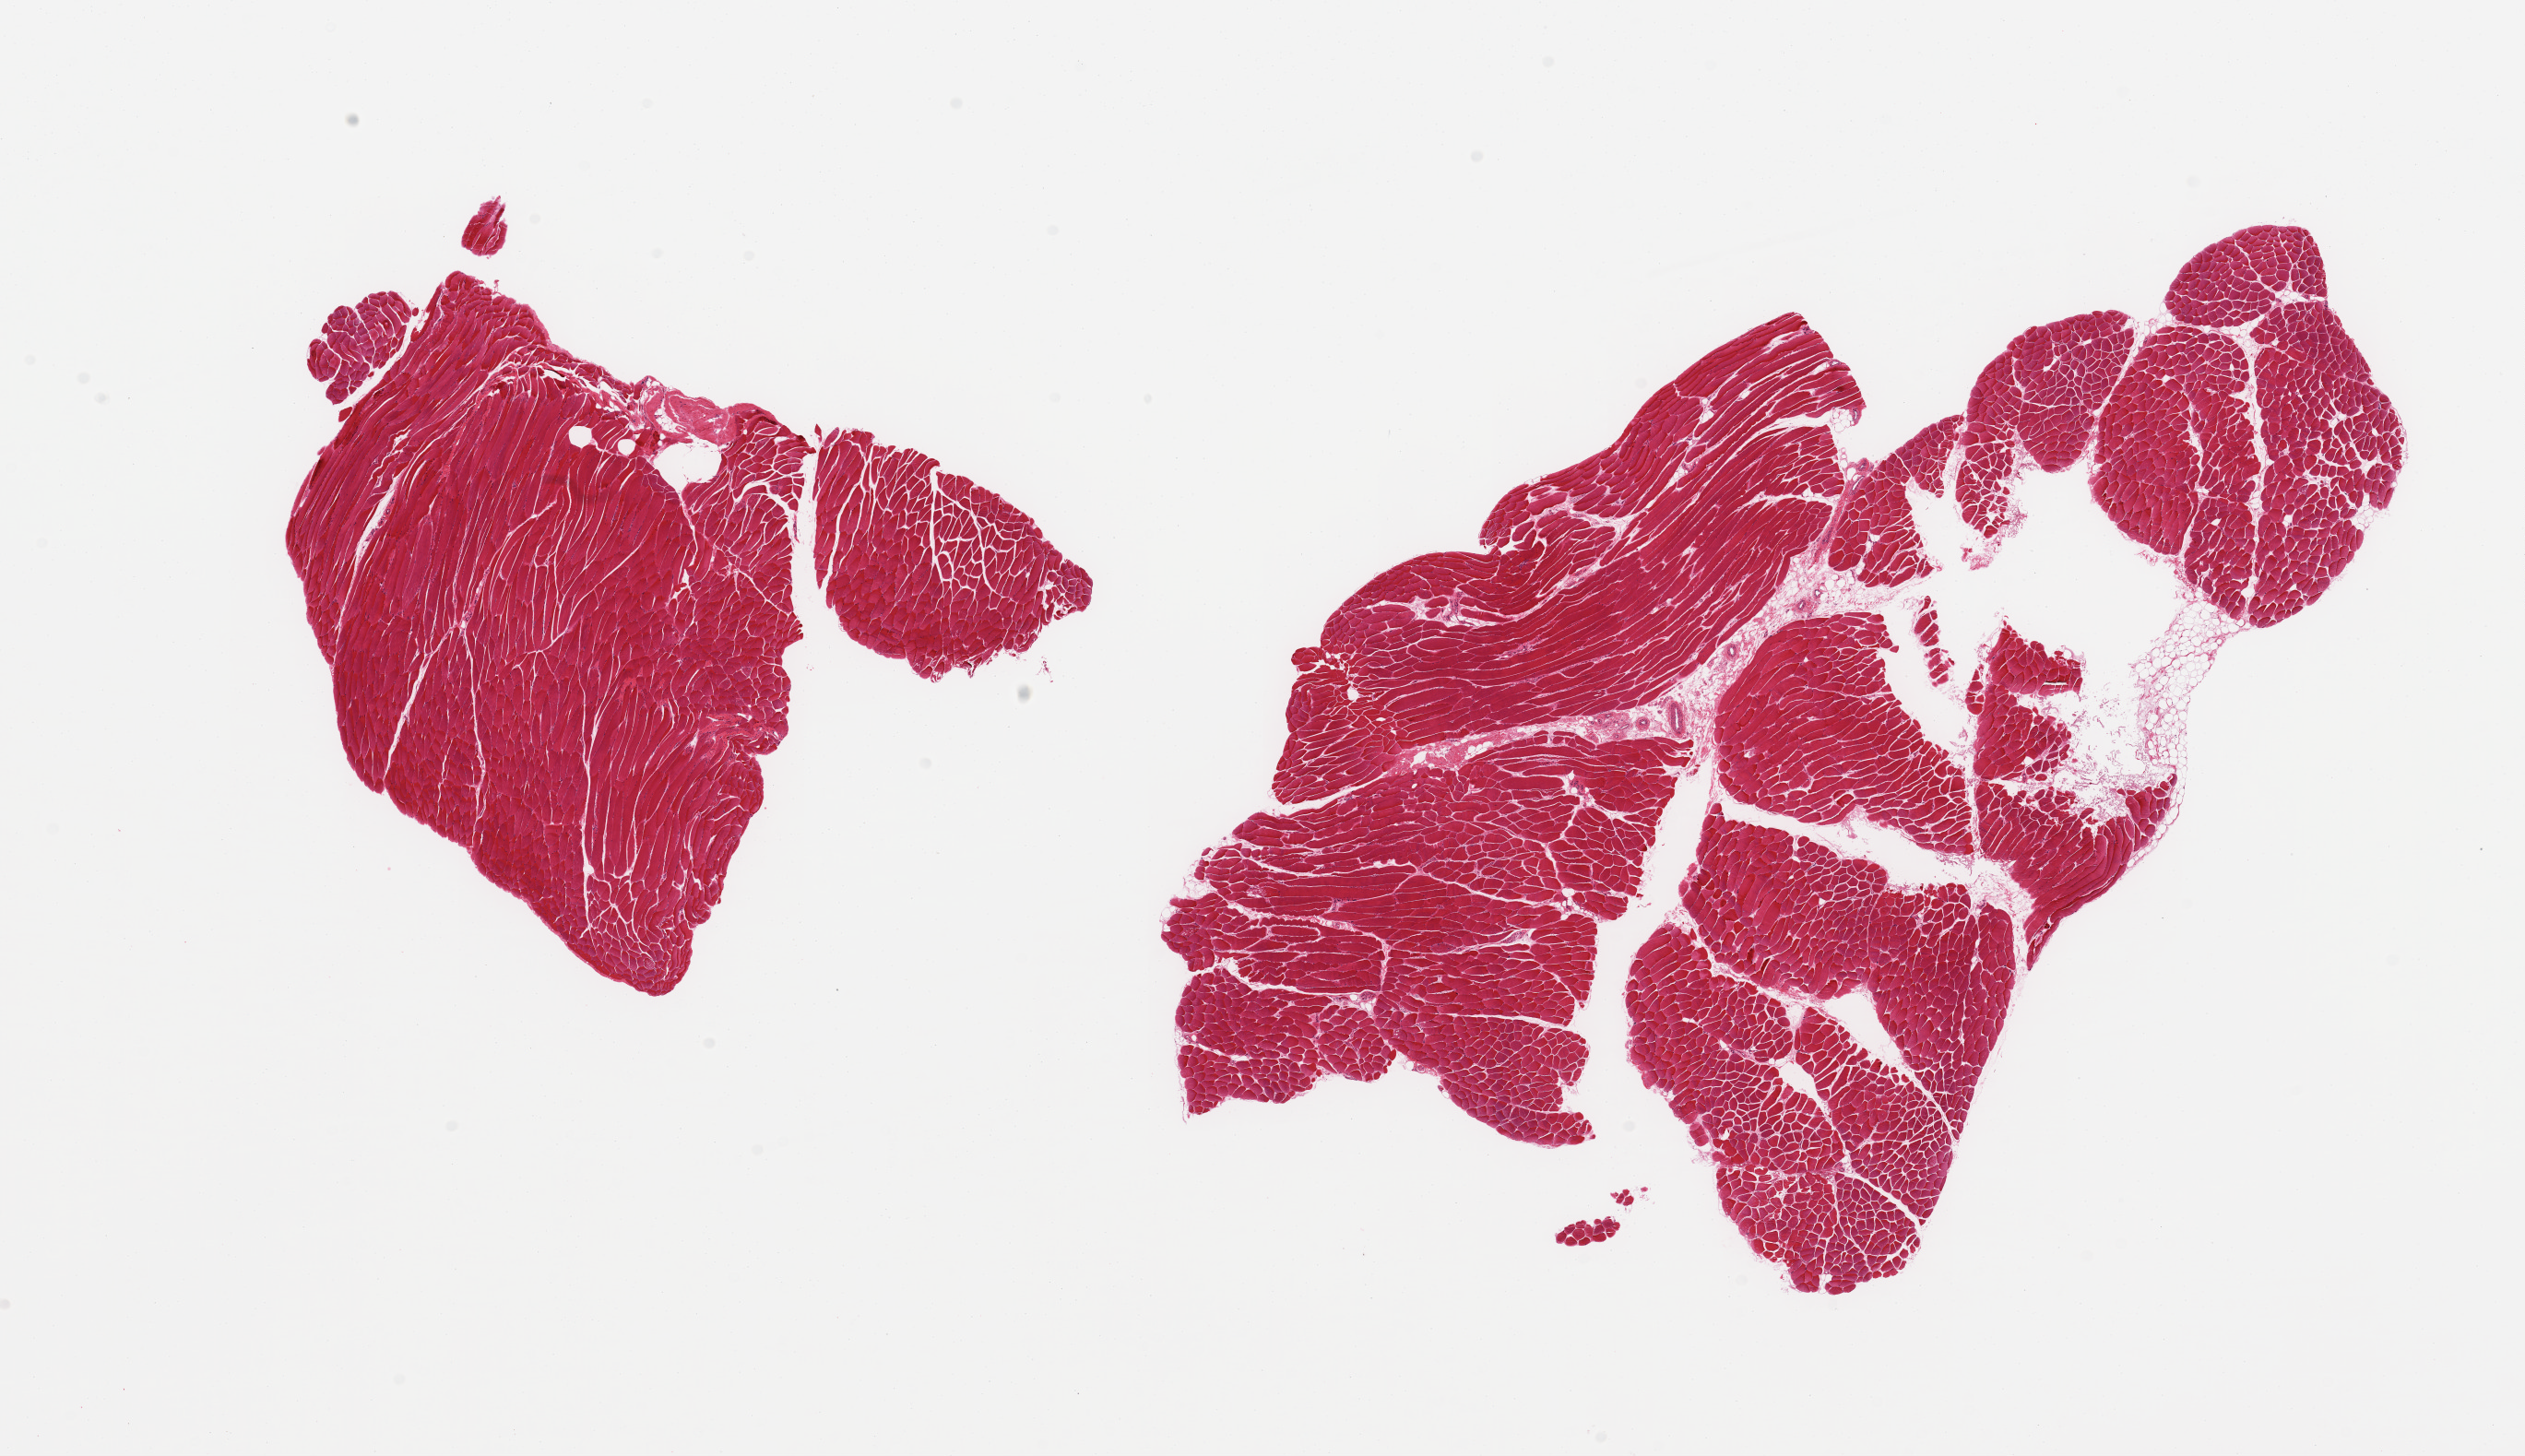
Digitized haematoxylin and eosin-stained section, low-resolution overview of the scanned area, about 21.7 x 12.5 mm, PAXgene-fixed paraffin-embedded (PFPE) section, target tissue: skeletal muscle, tissue donor sample. Donor sex: female.
Review note (as recorded): 2 pieces, ~10% interstitial fat.